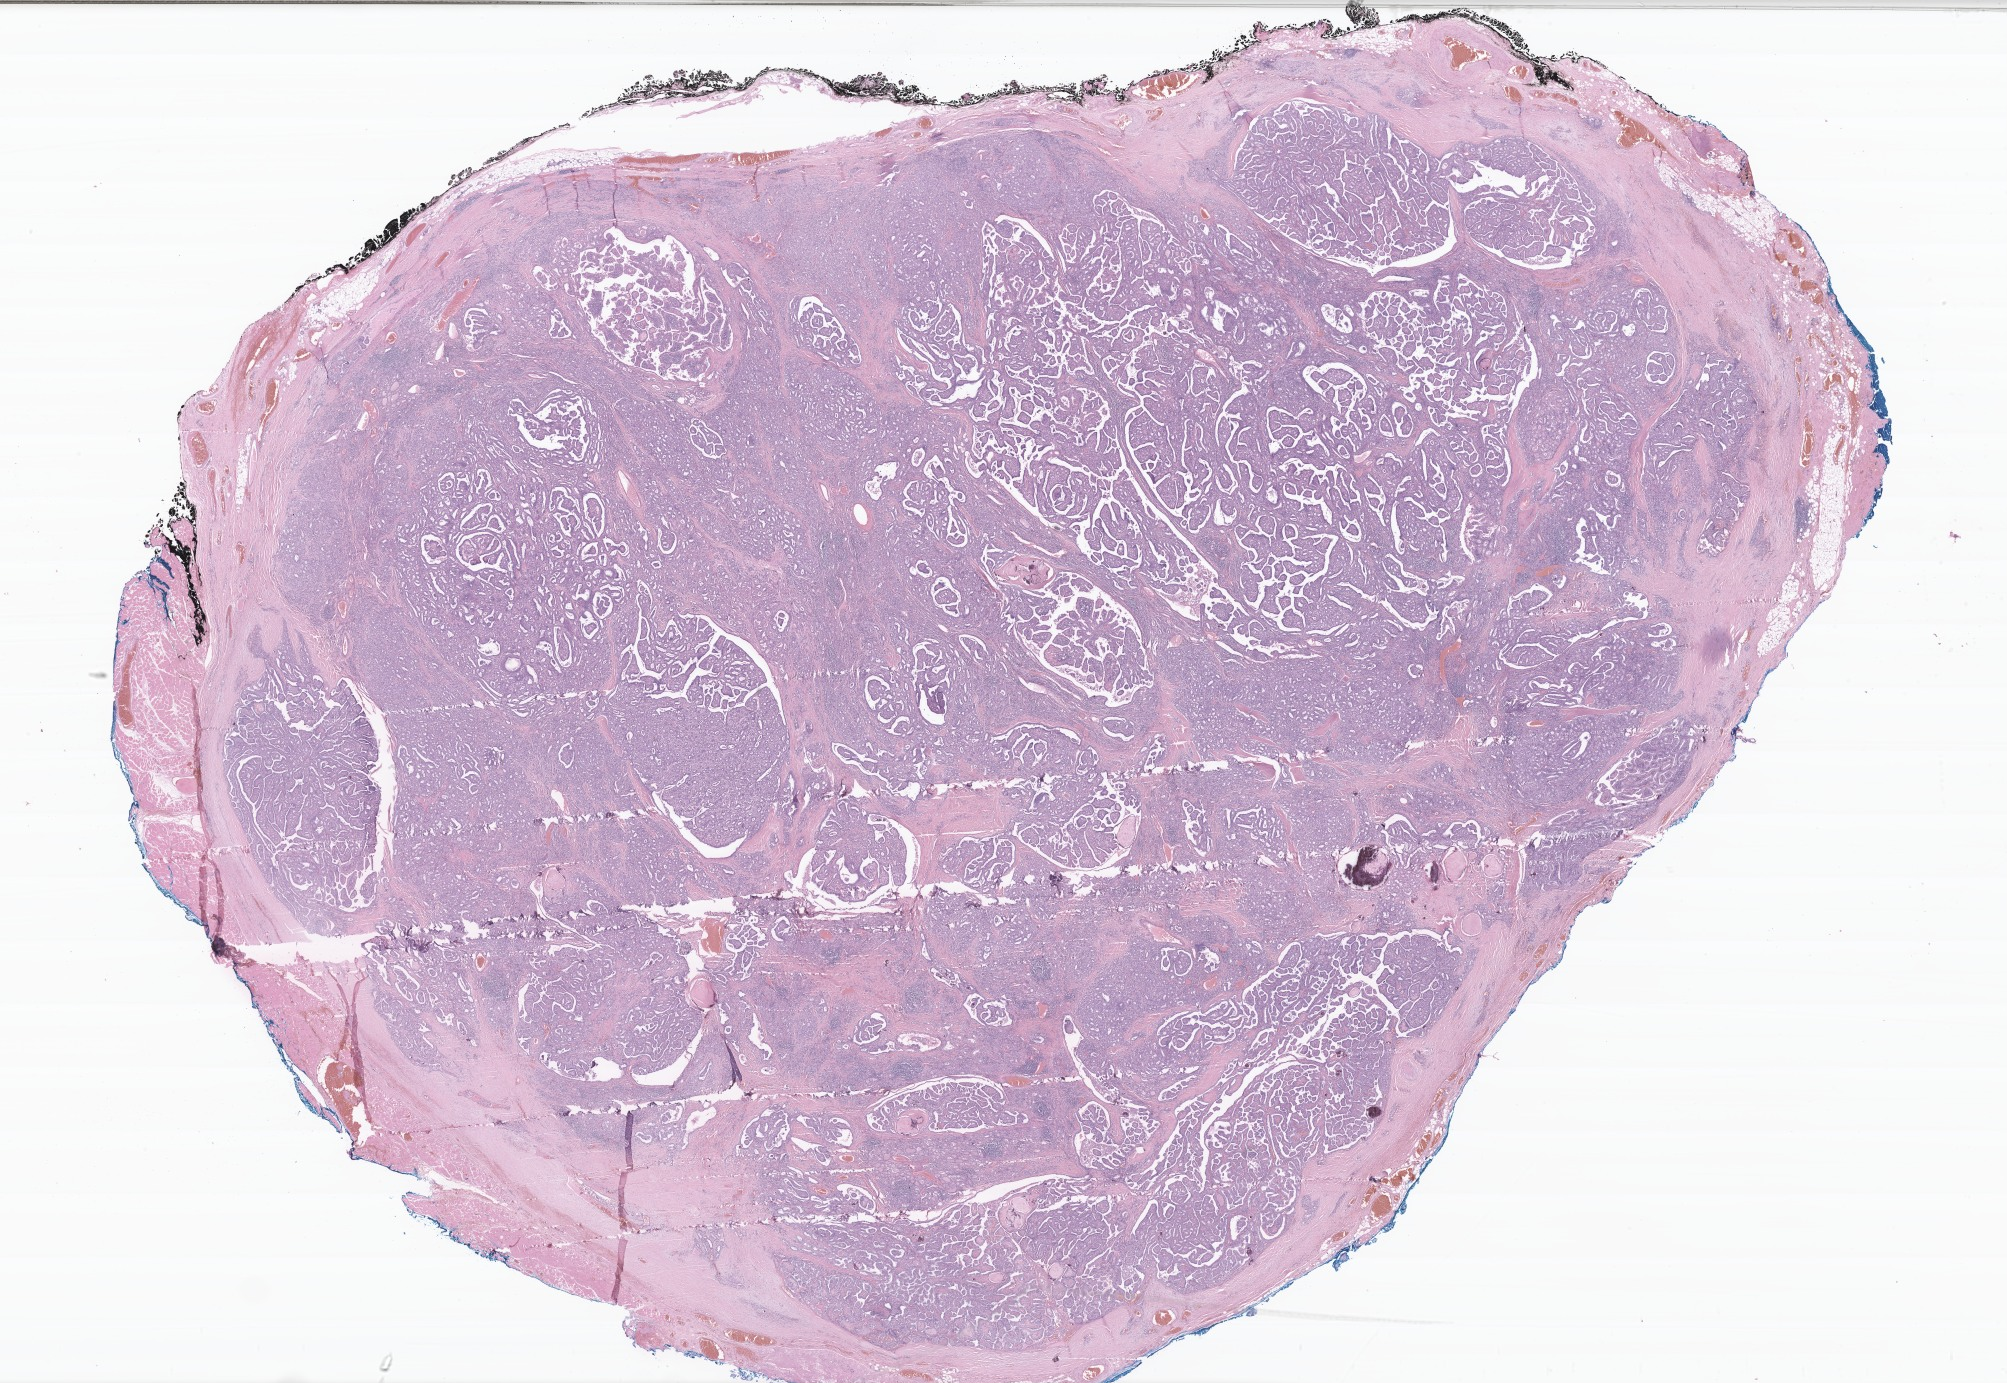
Whole-slide image, haematoxylin and eosin stain of tumor tissue from the thyroid — shown as a low-resolution overview of the whole scanned area (about 33.8 x 23.3 mm), formalin-fixed, paraffin-embedded (FFPE) tissue. Female patient, age 212 months (17 years 8 months).
Diagnosis: Papillary carcinoma, NOS.